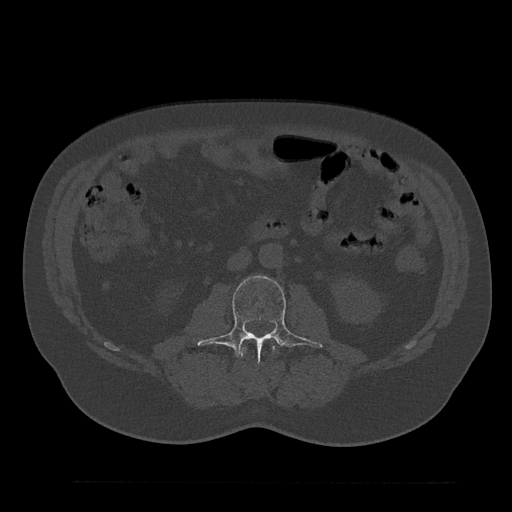
CT including the spine, one axial slice. Slice 43 of 797 in the series (ordered by position). Reconstruction kernel Br40s/3. 120 kVp. Bone window (W 1800 / L 400 HU). 0.5 mm slice thickness. 512 × 512 image matrix, field of view 430 × 430 mm. Male patient, age 61 years. From the clinical record (not read from this slice): primary cancer: prostate.
Annotated regions visible in this slice (semi-automatic segmentation, software-assisted and operator-edited):
- L2 vertebra: bounding box (x1, y1, x2, y2) in pixels: (241, 345, 276, 357)
- L3 vertebra: (197, 276, 323, 358)